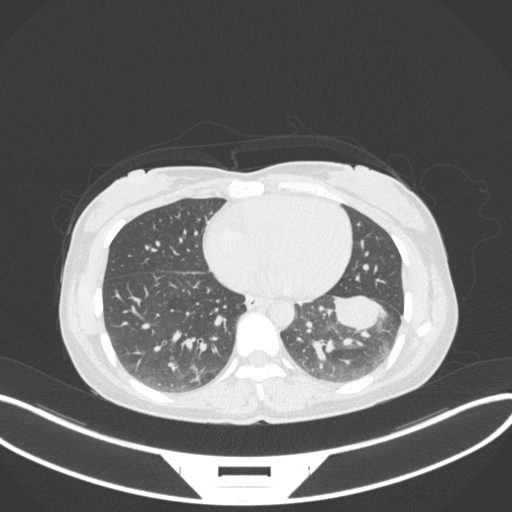
Chest CT, one axial slice. Position 134 of 361 along the scan axis. Reconstruction kernel B31f. Lung window (W 1500 / L -600 HU). 1 mm slice thickness. 512 × 512 image matrix, field of view 400 × 400 mm. Patient: female, 41 years. From the clinical record (not read from this slice): clinical TNM (as recorded): T2a N3 M1b.
Structures marked on this image (rectangle marked by the reading radiologist):
- lung tumour (recorded histology: adenocarcinoma): bounding box <330,292,396,339> (left, top, right, bottom; pixels)